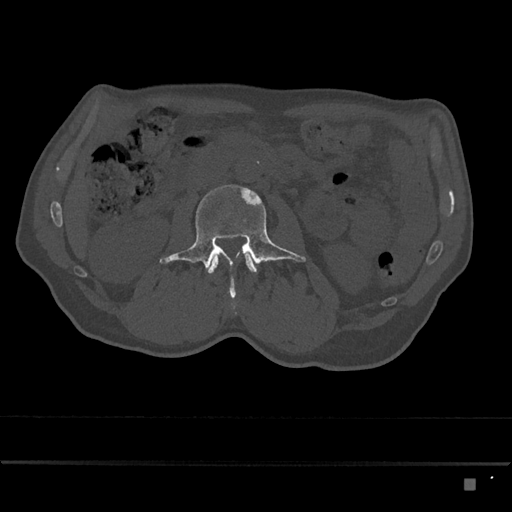
CT including the spine, one axial slice; position 423 of 797 along the scan axis; bone window (W 1800 / L 400 HU); 0.5 mm slice thickness; 512 × 512 image matrix, field of view 390 × 390 mm. Patient: male, 72 years. From the clinical record (not read from this slice): primary cancer: prostate.
Annotated regions visible in this slice (semi-automatic segmentation, software-assisted and operator-edited):
- L2 vertebra: box from (x=208, y=253) to (x=257, y=274) px
- L3 vertebra: (x=159, y=184)–(x=306, y=299)